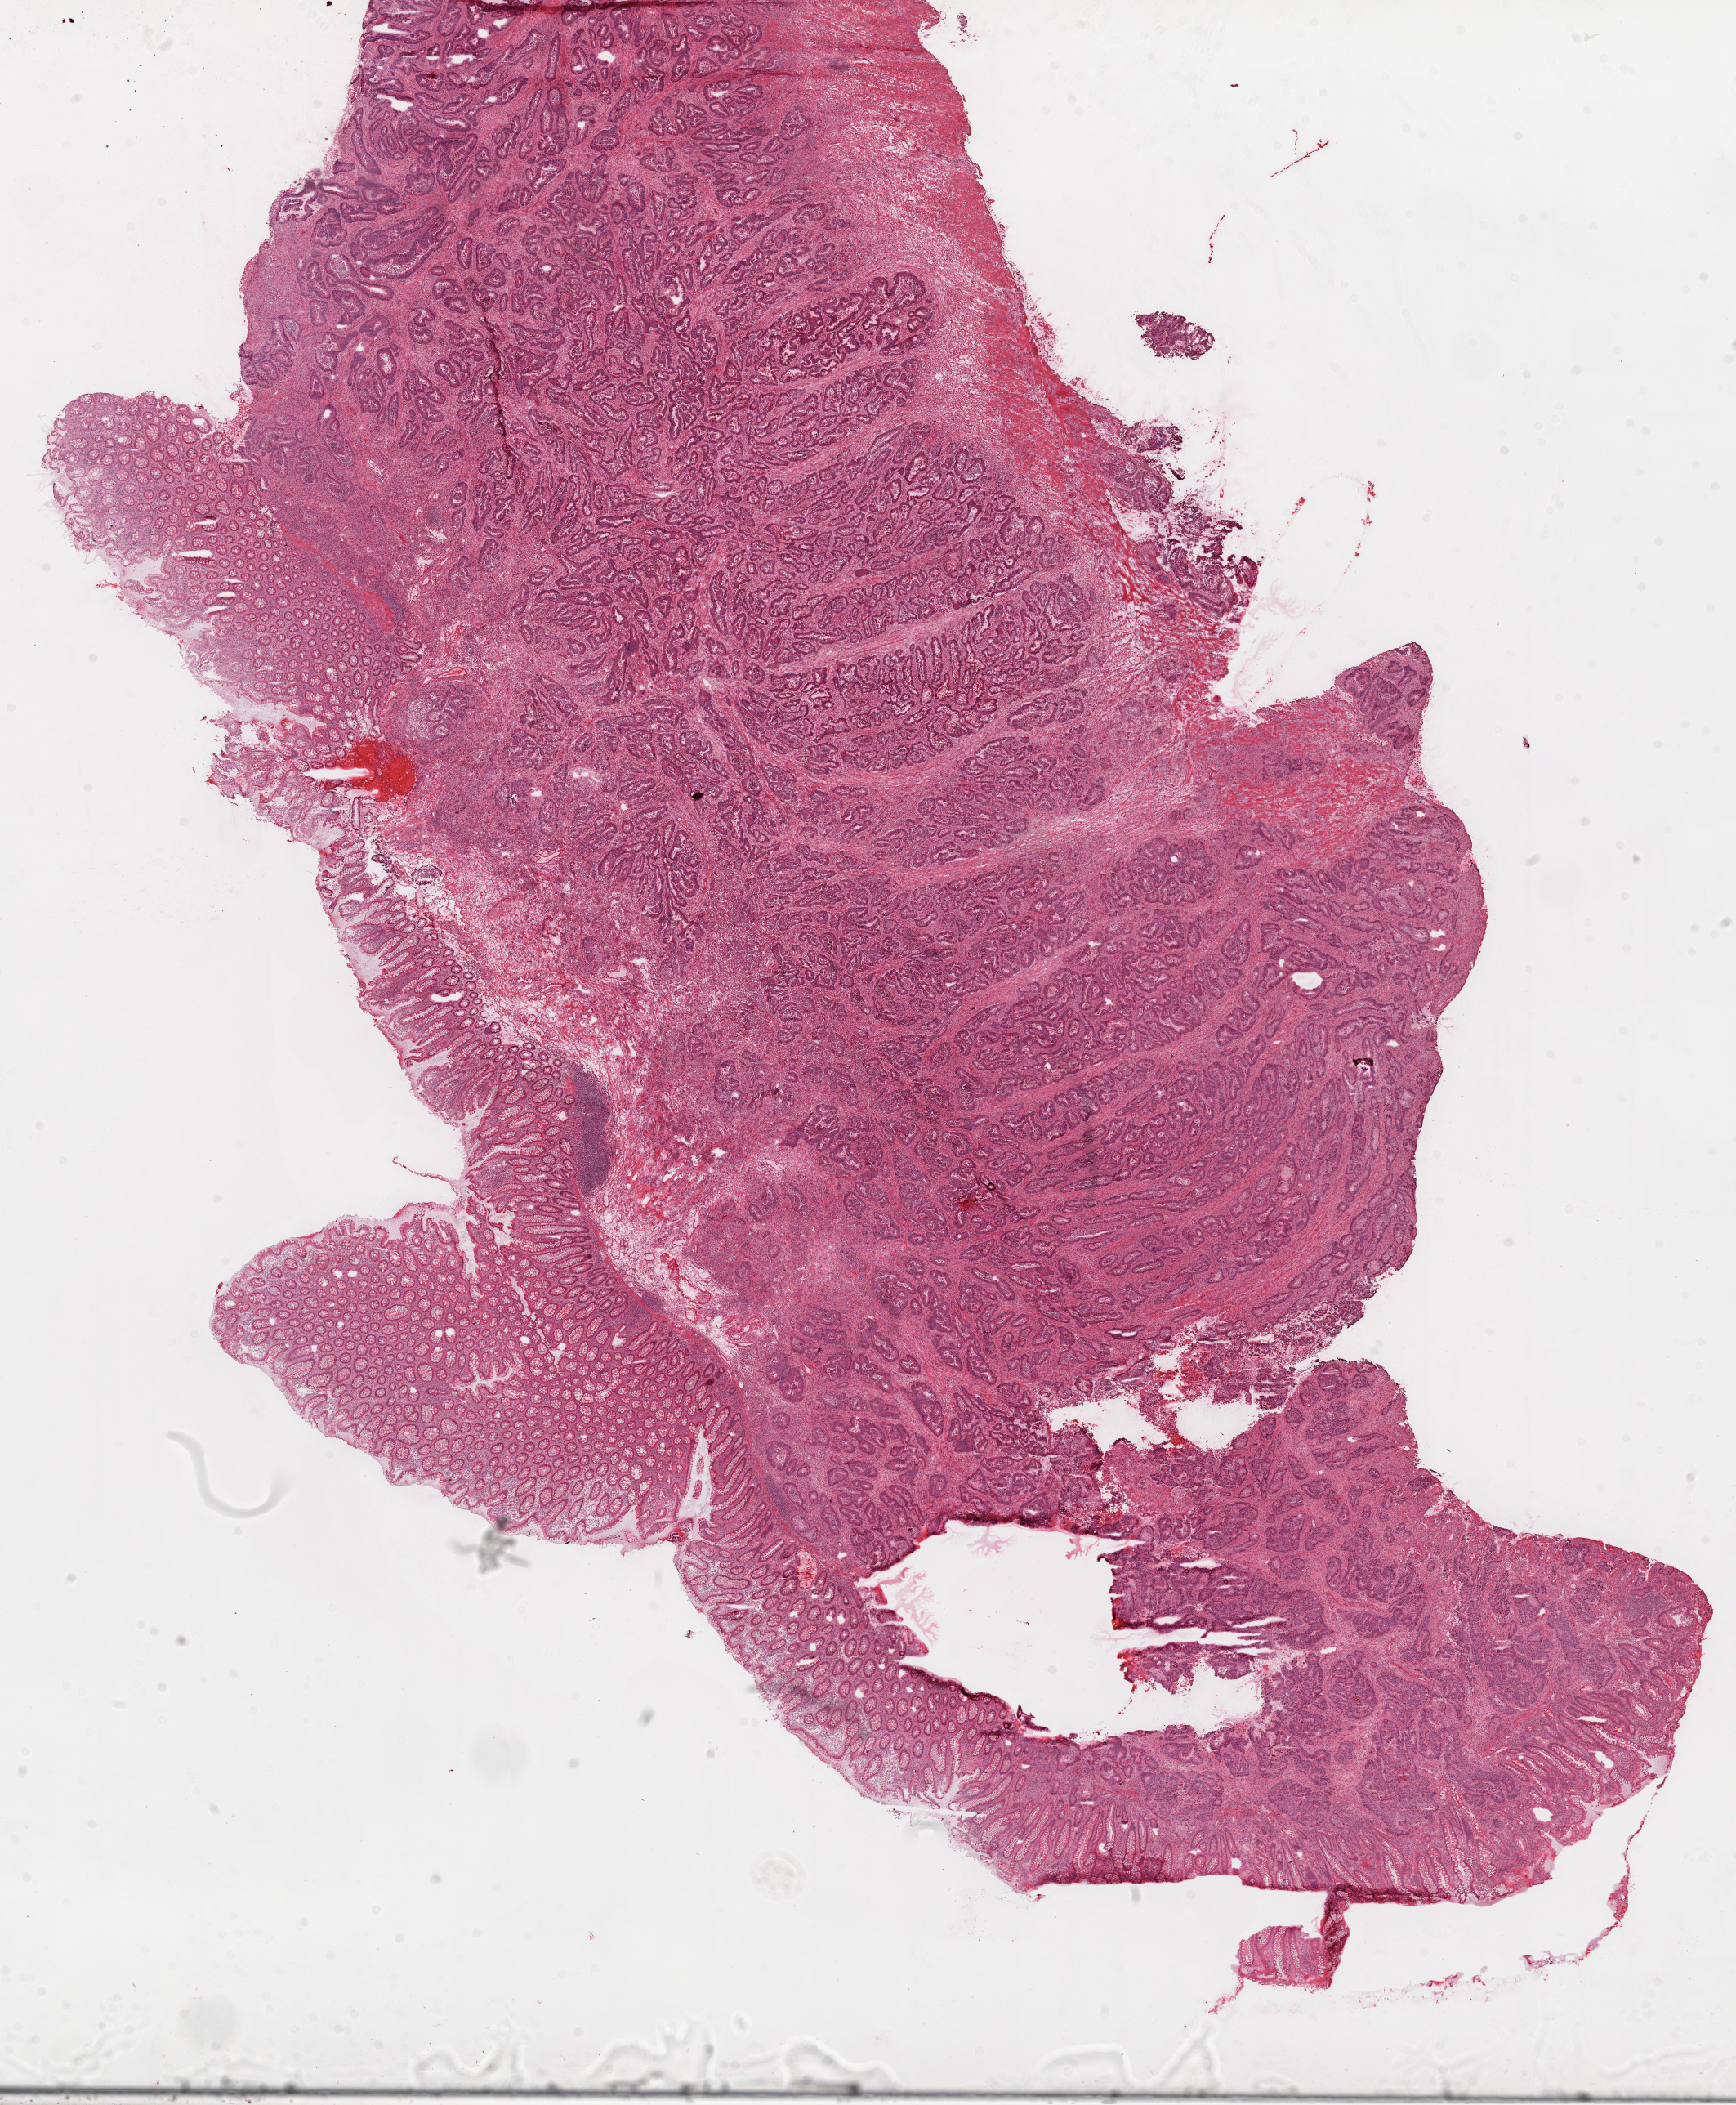
Whole-slide histology image, Hematoxylin and eosin (H&E) stained, shown as a low-resolution overview of the whole scanned area (about 17.1 x 20.7 mm, acquisition: 20x scan), frozen section from the top of the tissue portion, sample: primary tumour, colon. Male patient; age at initial diagnosis 58 years. Slide review estimates, as recorded: tumour cells 63%, tumour nuclei 75%.
Diagnosis: Adenocarcinoma, NOS.